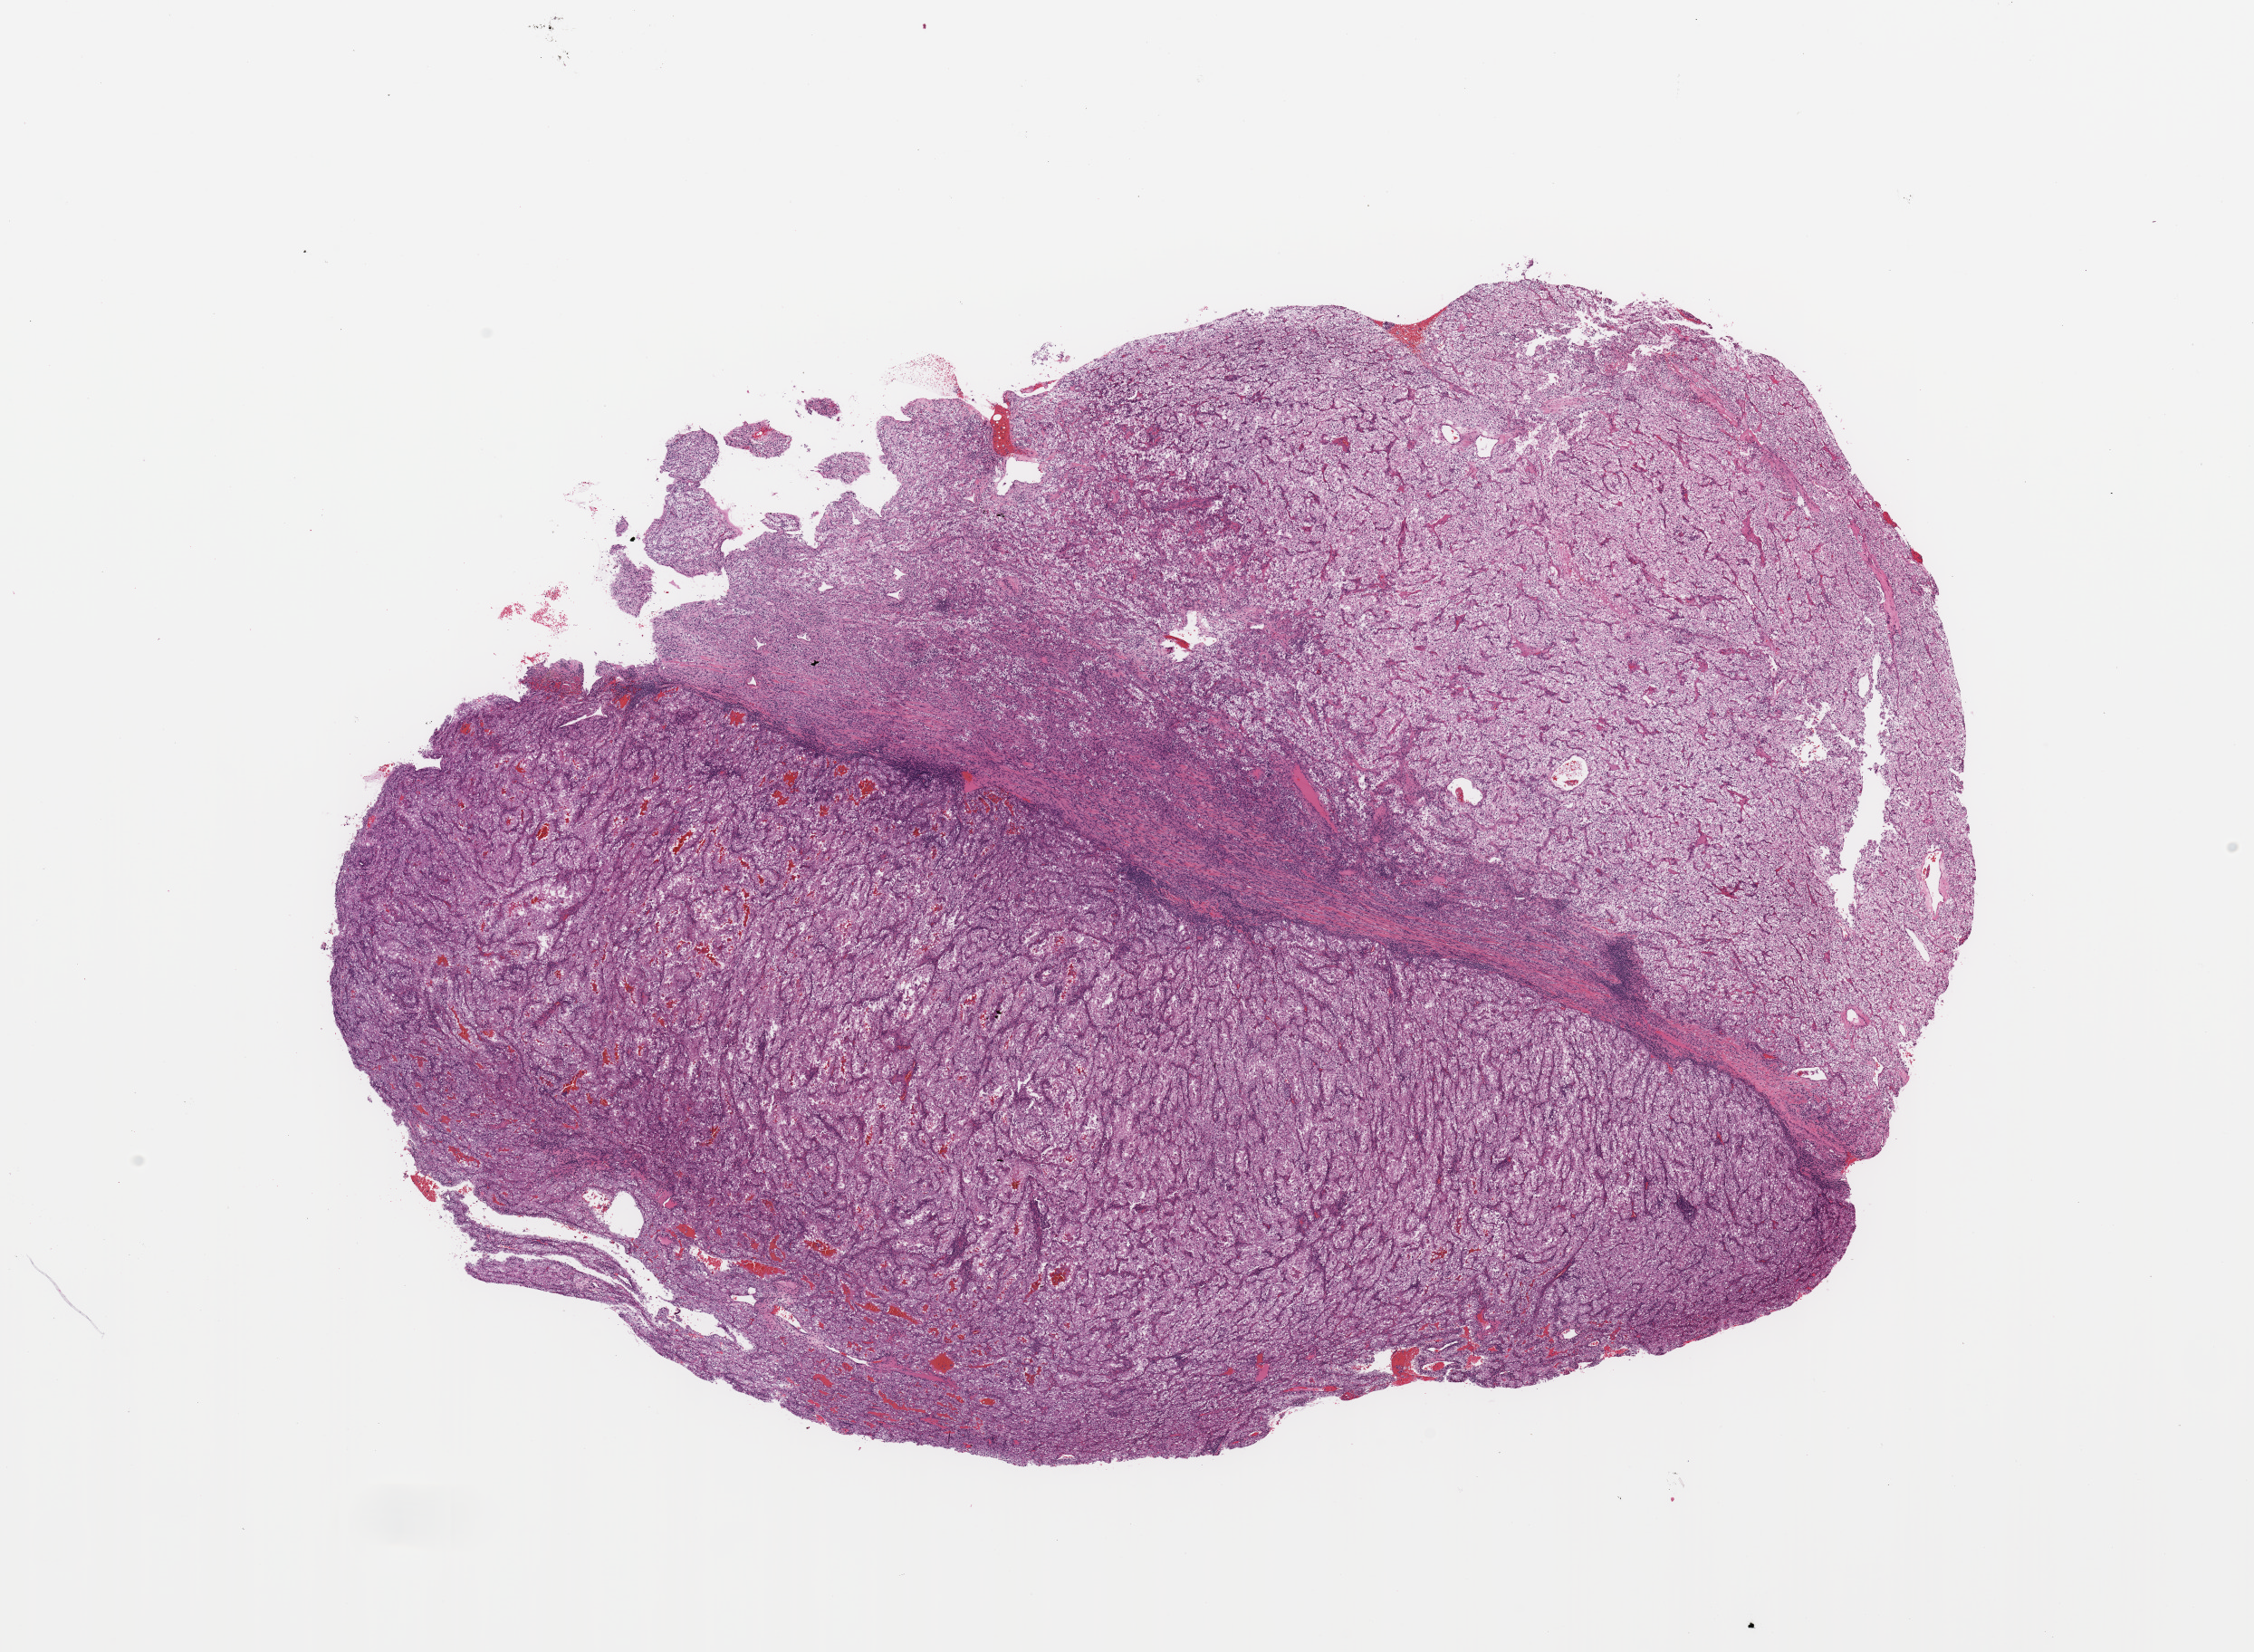
Digitized Hematoxylin and eosin (H&E) stained tissue section (whole slide) — a low-resolution overview of the entire scanned area, about 19.7 x 14.4 mm. Tumour tissue sample, sampled site: kidney. Patient: male, age 40 years. Histologic grade: G3 (poorly differentiated). Slide review estimates, as recorded: tumour nuclei 85%, necrosis 5%.
AJCC pathologic stage: IV. Diagnosis: Renal cell carcinoma, NOS.